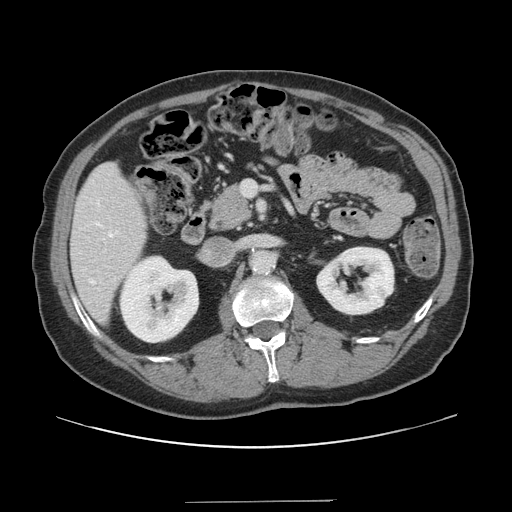
Contrast-enhanced abdominal CT, one axial slice; slice 66 of 151 in the series (ordered by position); 120 kVp; intravenous contrast given; soft-tissue window (W 400 / L 40 HU); 512 × 512 image matrix, field of view 399 × 399 mm. Male patient, age 63 years. Case-level facts recorded for this patient, not image findings: diagnosis: colorectal cancer liver metastases, imaged before liver resection; multiple liver metastases: no; largest metastasis: 2.1 cm; chemotherapy before resection: no.
Annotated regions visible in this slice (manually delineated by an expert):
- hepatic veins: bounding box <90,232,113,284> (left, top, right, bottom; pixels)
- liver: <72,164,146,321>
- planned liver remnant (the part of the liver to remain after resection): <72,164,147,322>
- portal vein (with intrahepatic branches): <104,181,257,252>